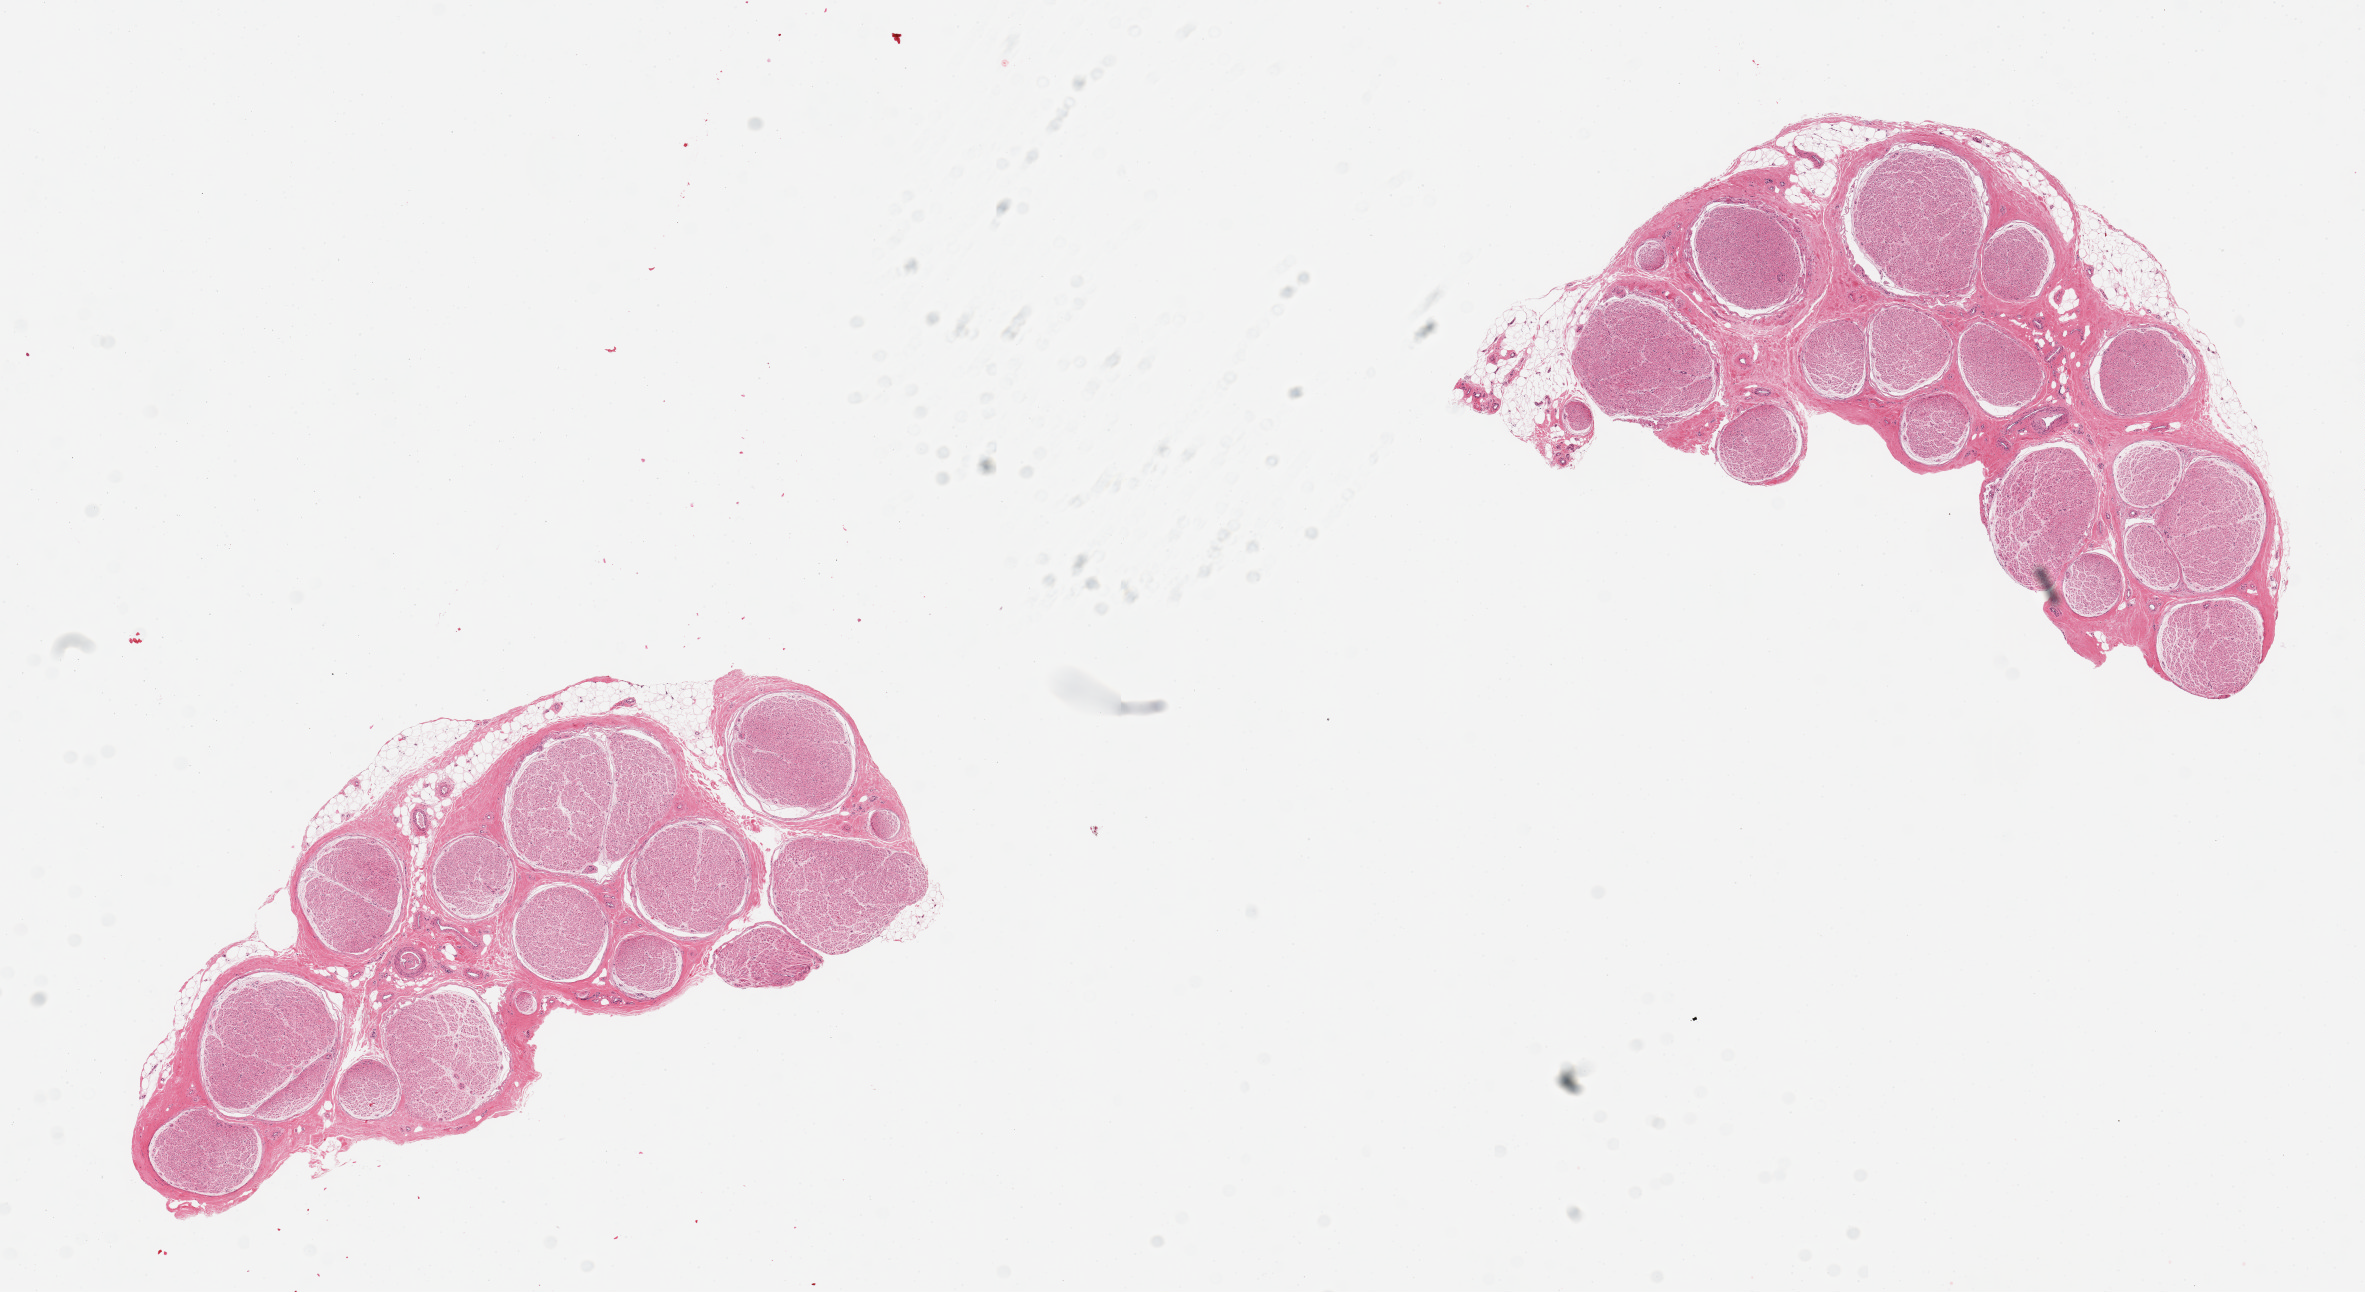
Digitized H&E-stained section, whole scanned area (about 18.7 x 10.2 mm) shown as a low-resolution overview, PAXgene-fixed, paraffin-embedded tissue, target tissue: tibial nerve, tissue donor sample. Donor sex: male.
* reviewer comment on this tissue sample: 2 pieces; 10% fat